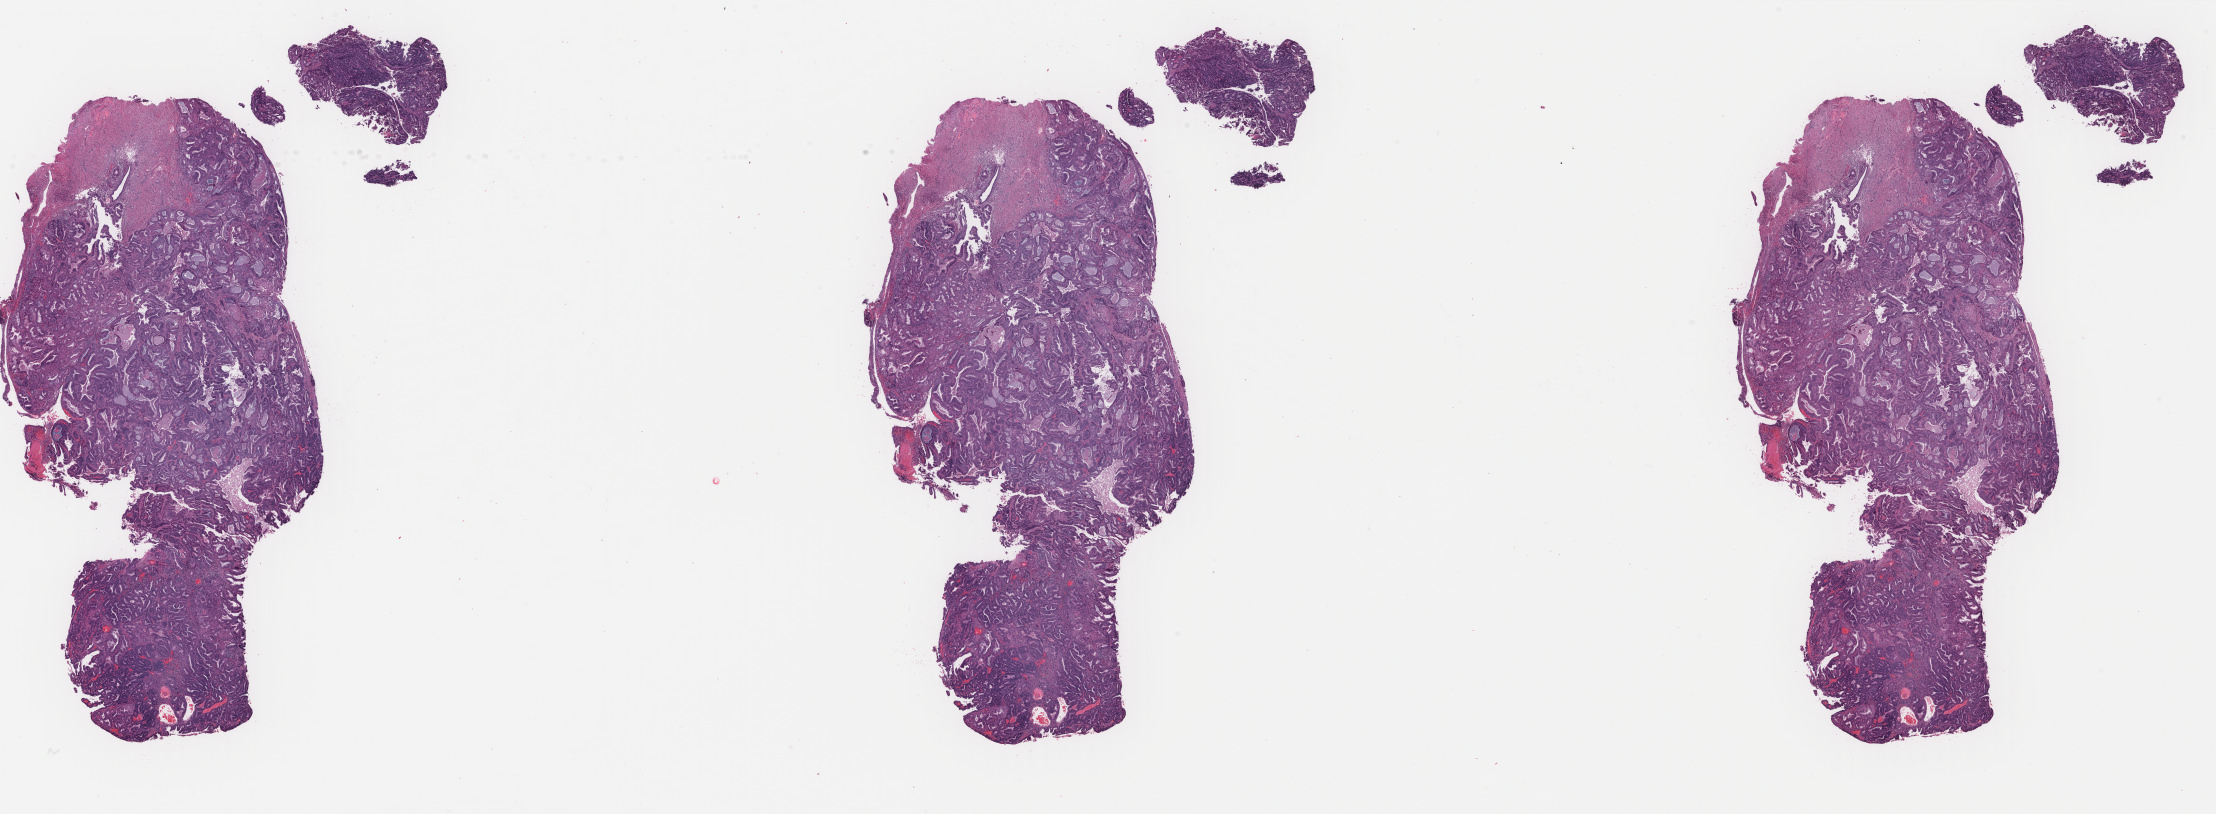
Digitized Hematoxylin and eosin (H&E) stained tissue section (whole slide), low-resolution overview of the scanned area, about 35.2 x 12.9 mm (acquisition: 40x scan); formalin-fixed paraffin-embedded (FFPE) diagnostic section; uterus, primary tumour sample. Patient: female, age at initial diagnosis 51 years. Histologic grade: G1 (well differentiated).
Lymph nodes positive (case pathology): 0 of 20 examined. Pathologic diagnosis: Endometrioid adenocarcinoma, NOS (endometrium). FIGO stage: IA.